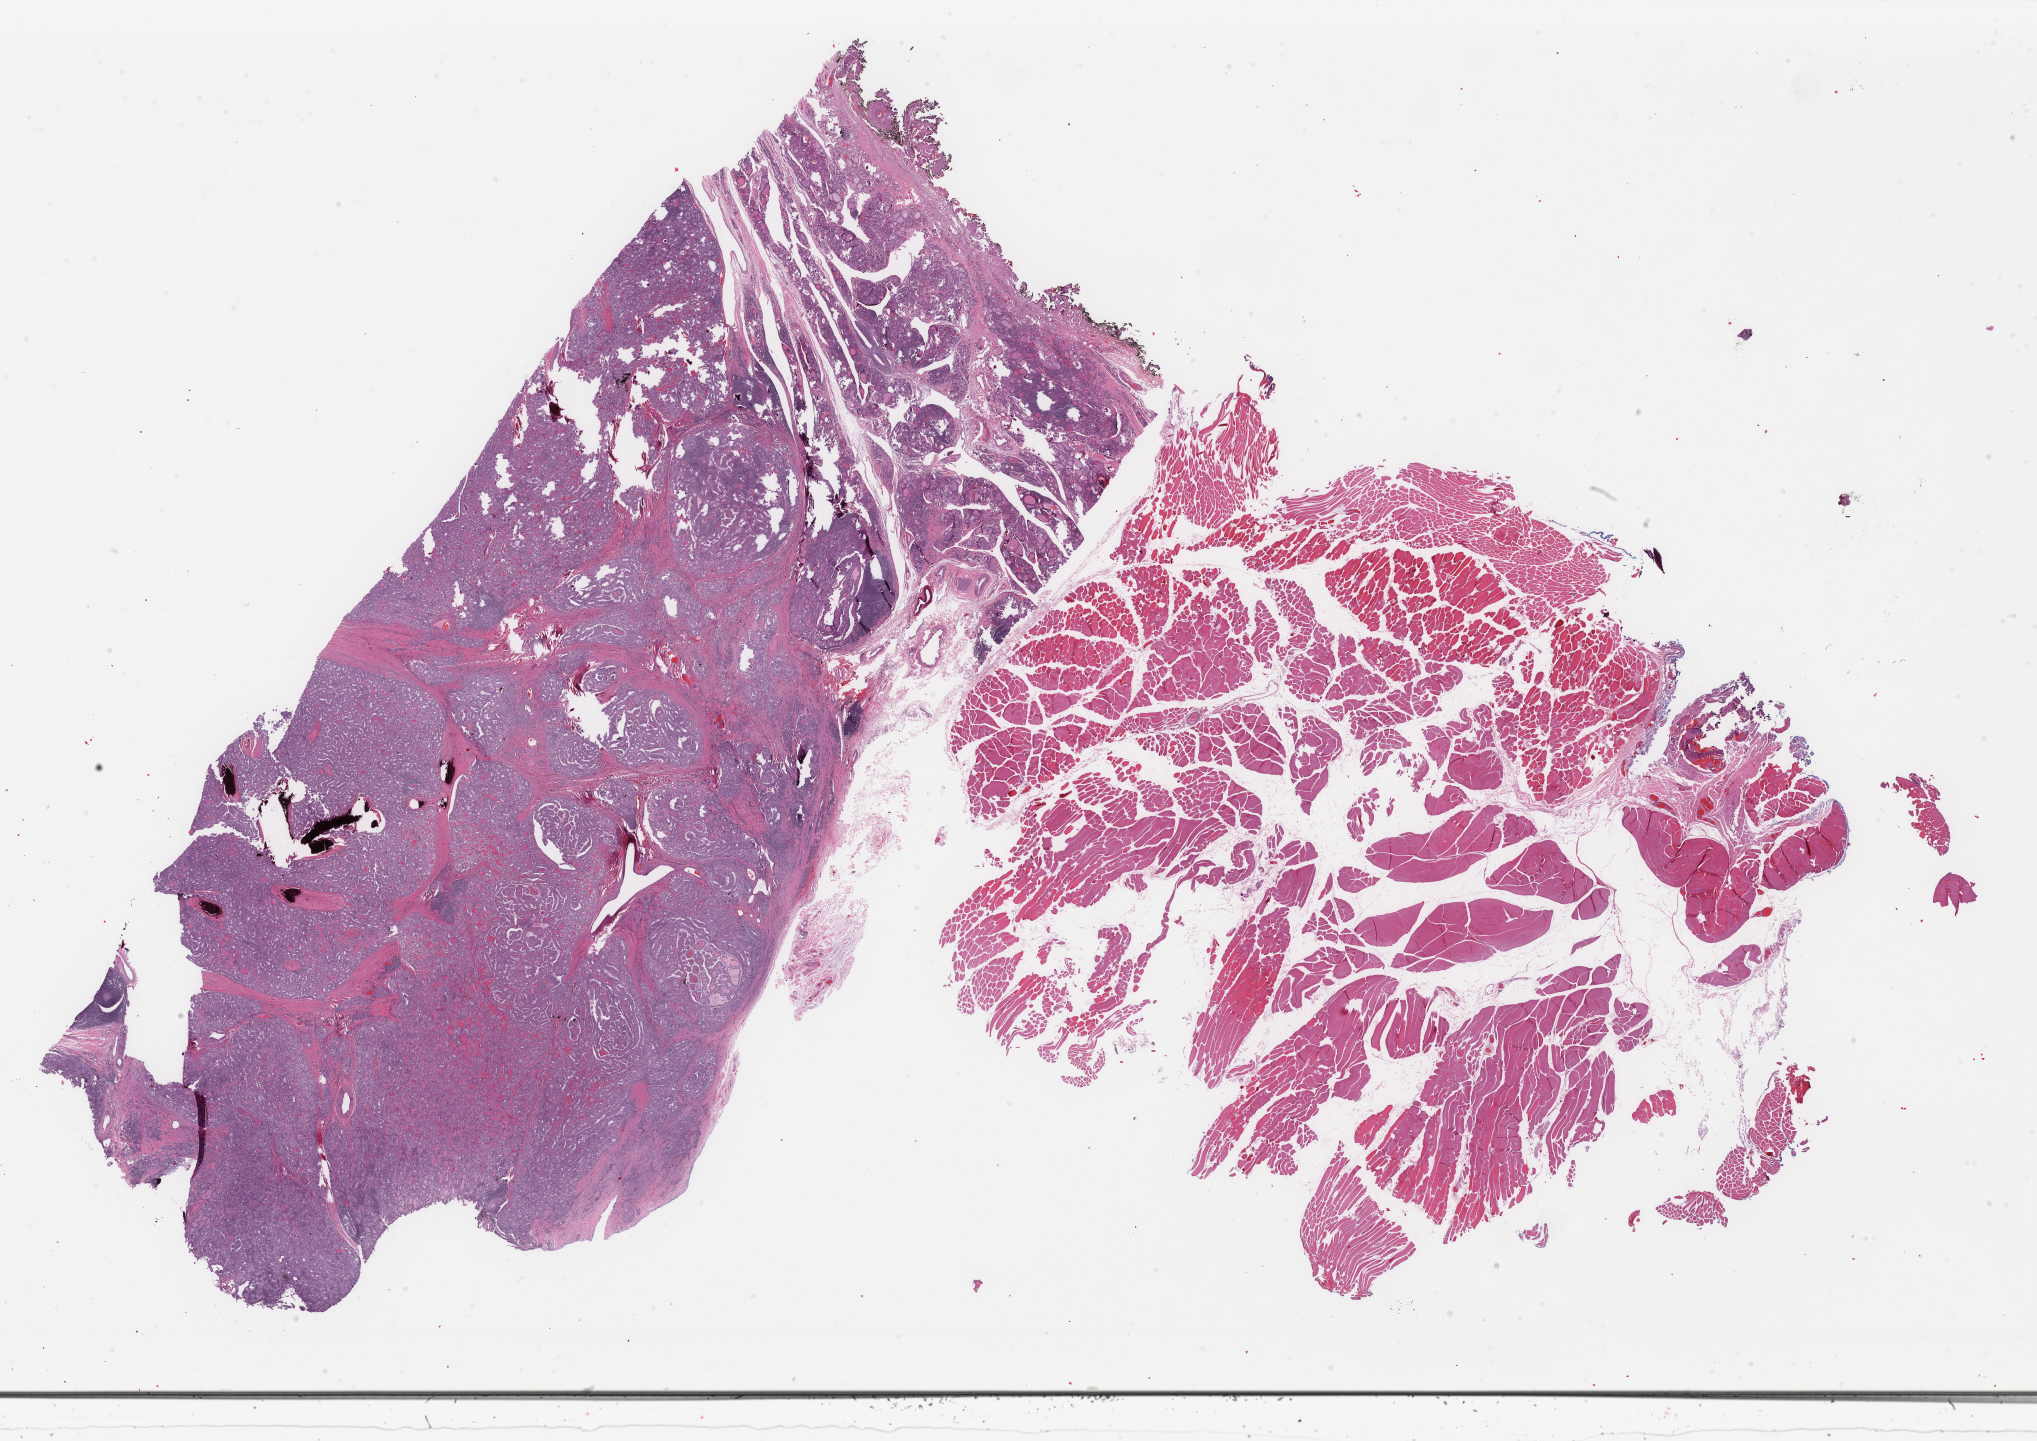
Whole-slide histology image, H&E-stained — a low-resolution overview of the entire scanned area, about 32.3 x 22.9 mm. FFPE section. Sample: primary tumour, thyroid. Male, age 51 years at initial diagnosis.
• pathologic diagnosis: Papillary adenocarcinoma, NOS (thyroid gland)
• AJCC pathologic stage: IVA (7th edition)
• lymph nodes positive (case pathology): 2 of 5 examined
• laterality: left